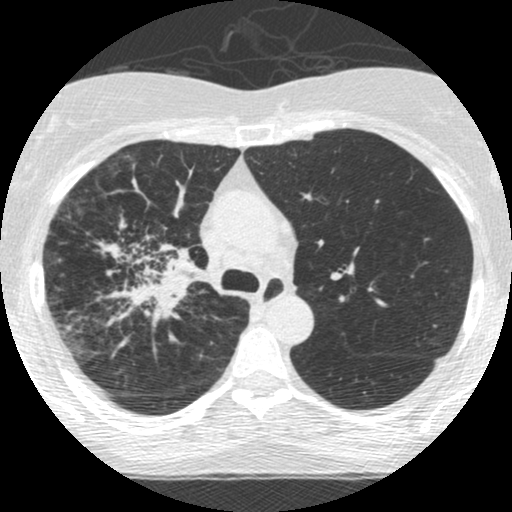
Low-dose screening chest CT, one axial slice. Slice 178 of 253 in the series (ordered by position). Reconstruction kernel STANDARD. Lung window (W 1500 / L -600 HU). 1.25 mm slice thickness. 512 × 512 image matrix, field of view 294 × 294 mm.
Structures marked on this image (expert manual segmentation):
- lesion 2 (tumor, hilum of right lung): bounding box <95,236,208,328> (left, top, right, bottom; pixels)